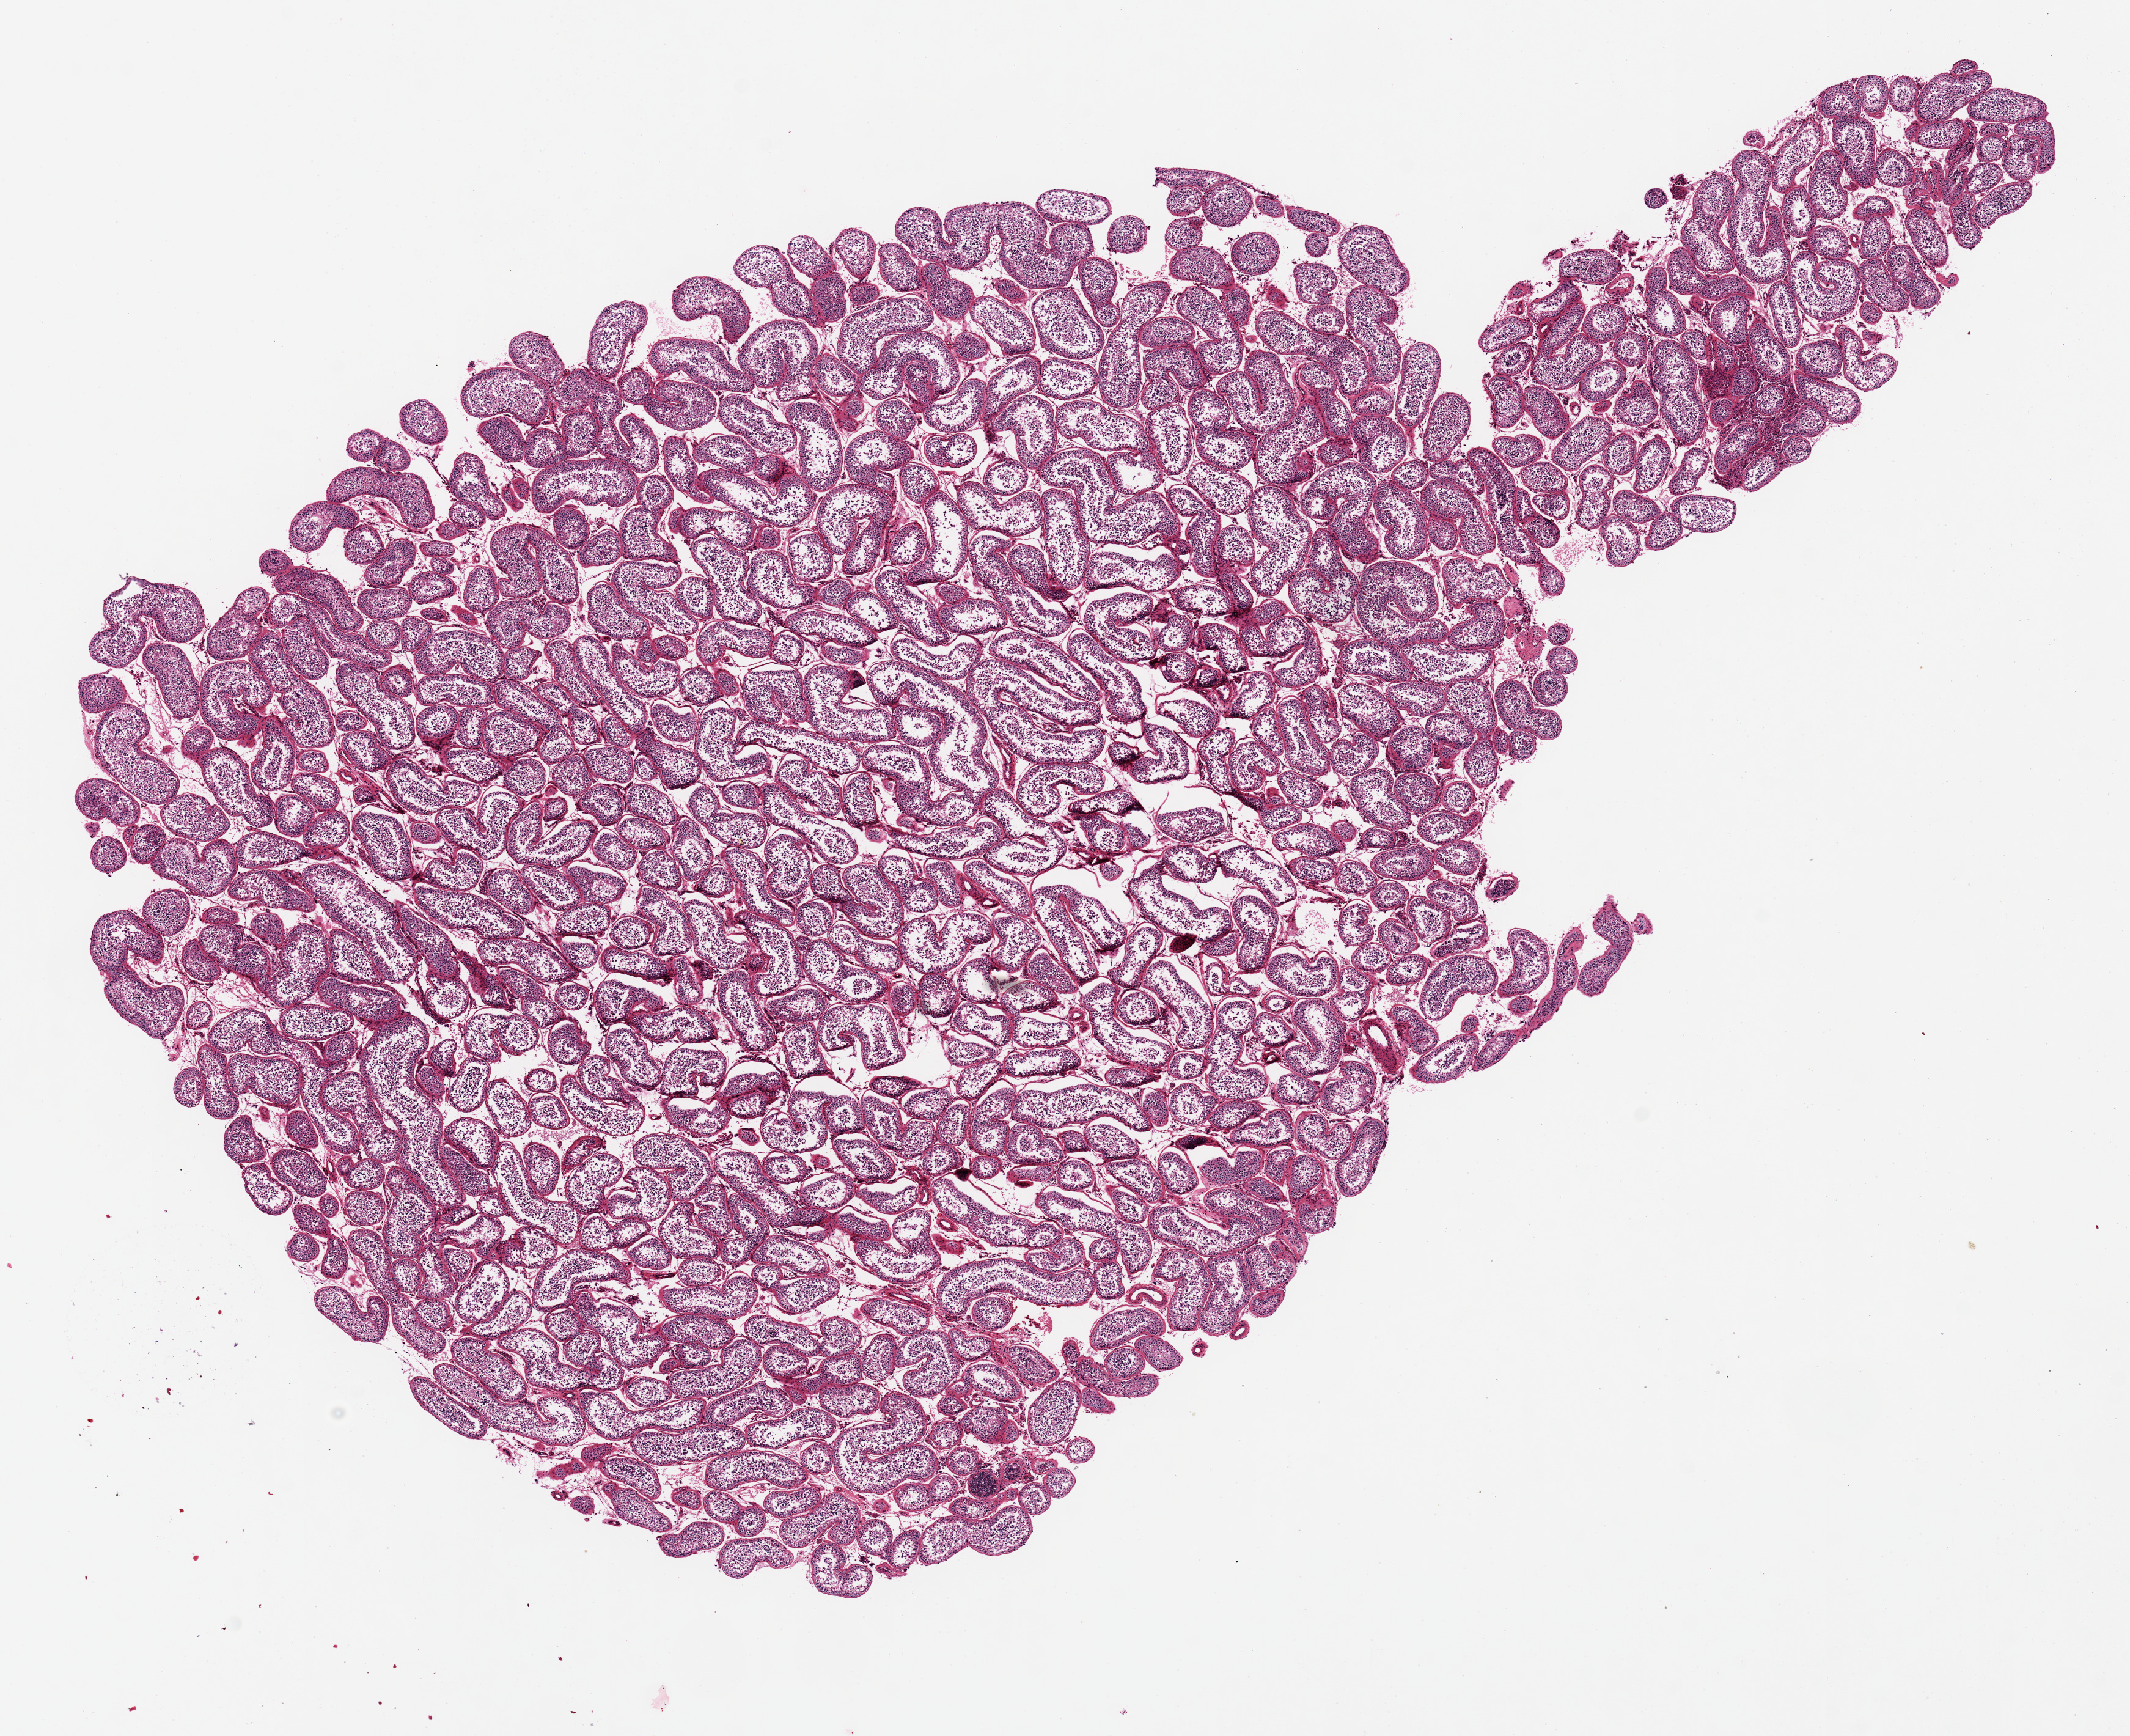
Digitized hematoxylin and eosin (H&E)-stained section, a low-resolution overview of the entire scanned area, about 13.8 x 11.2 mm, PAXgene-fixed, paraffin-embedded tissue, target tissue: testis, tissue donor sample. Donor: male.
Reviewer comment on this tissue sample: 13x8 mm.